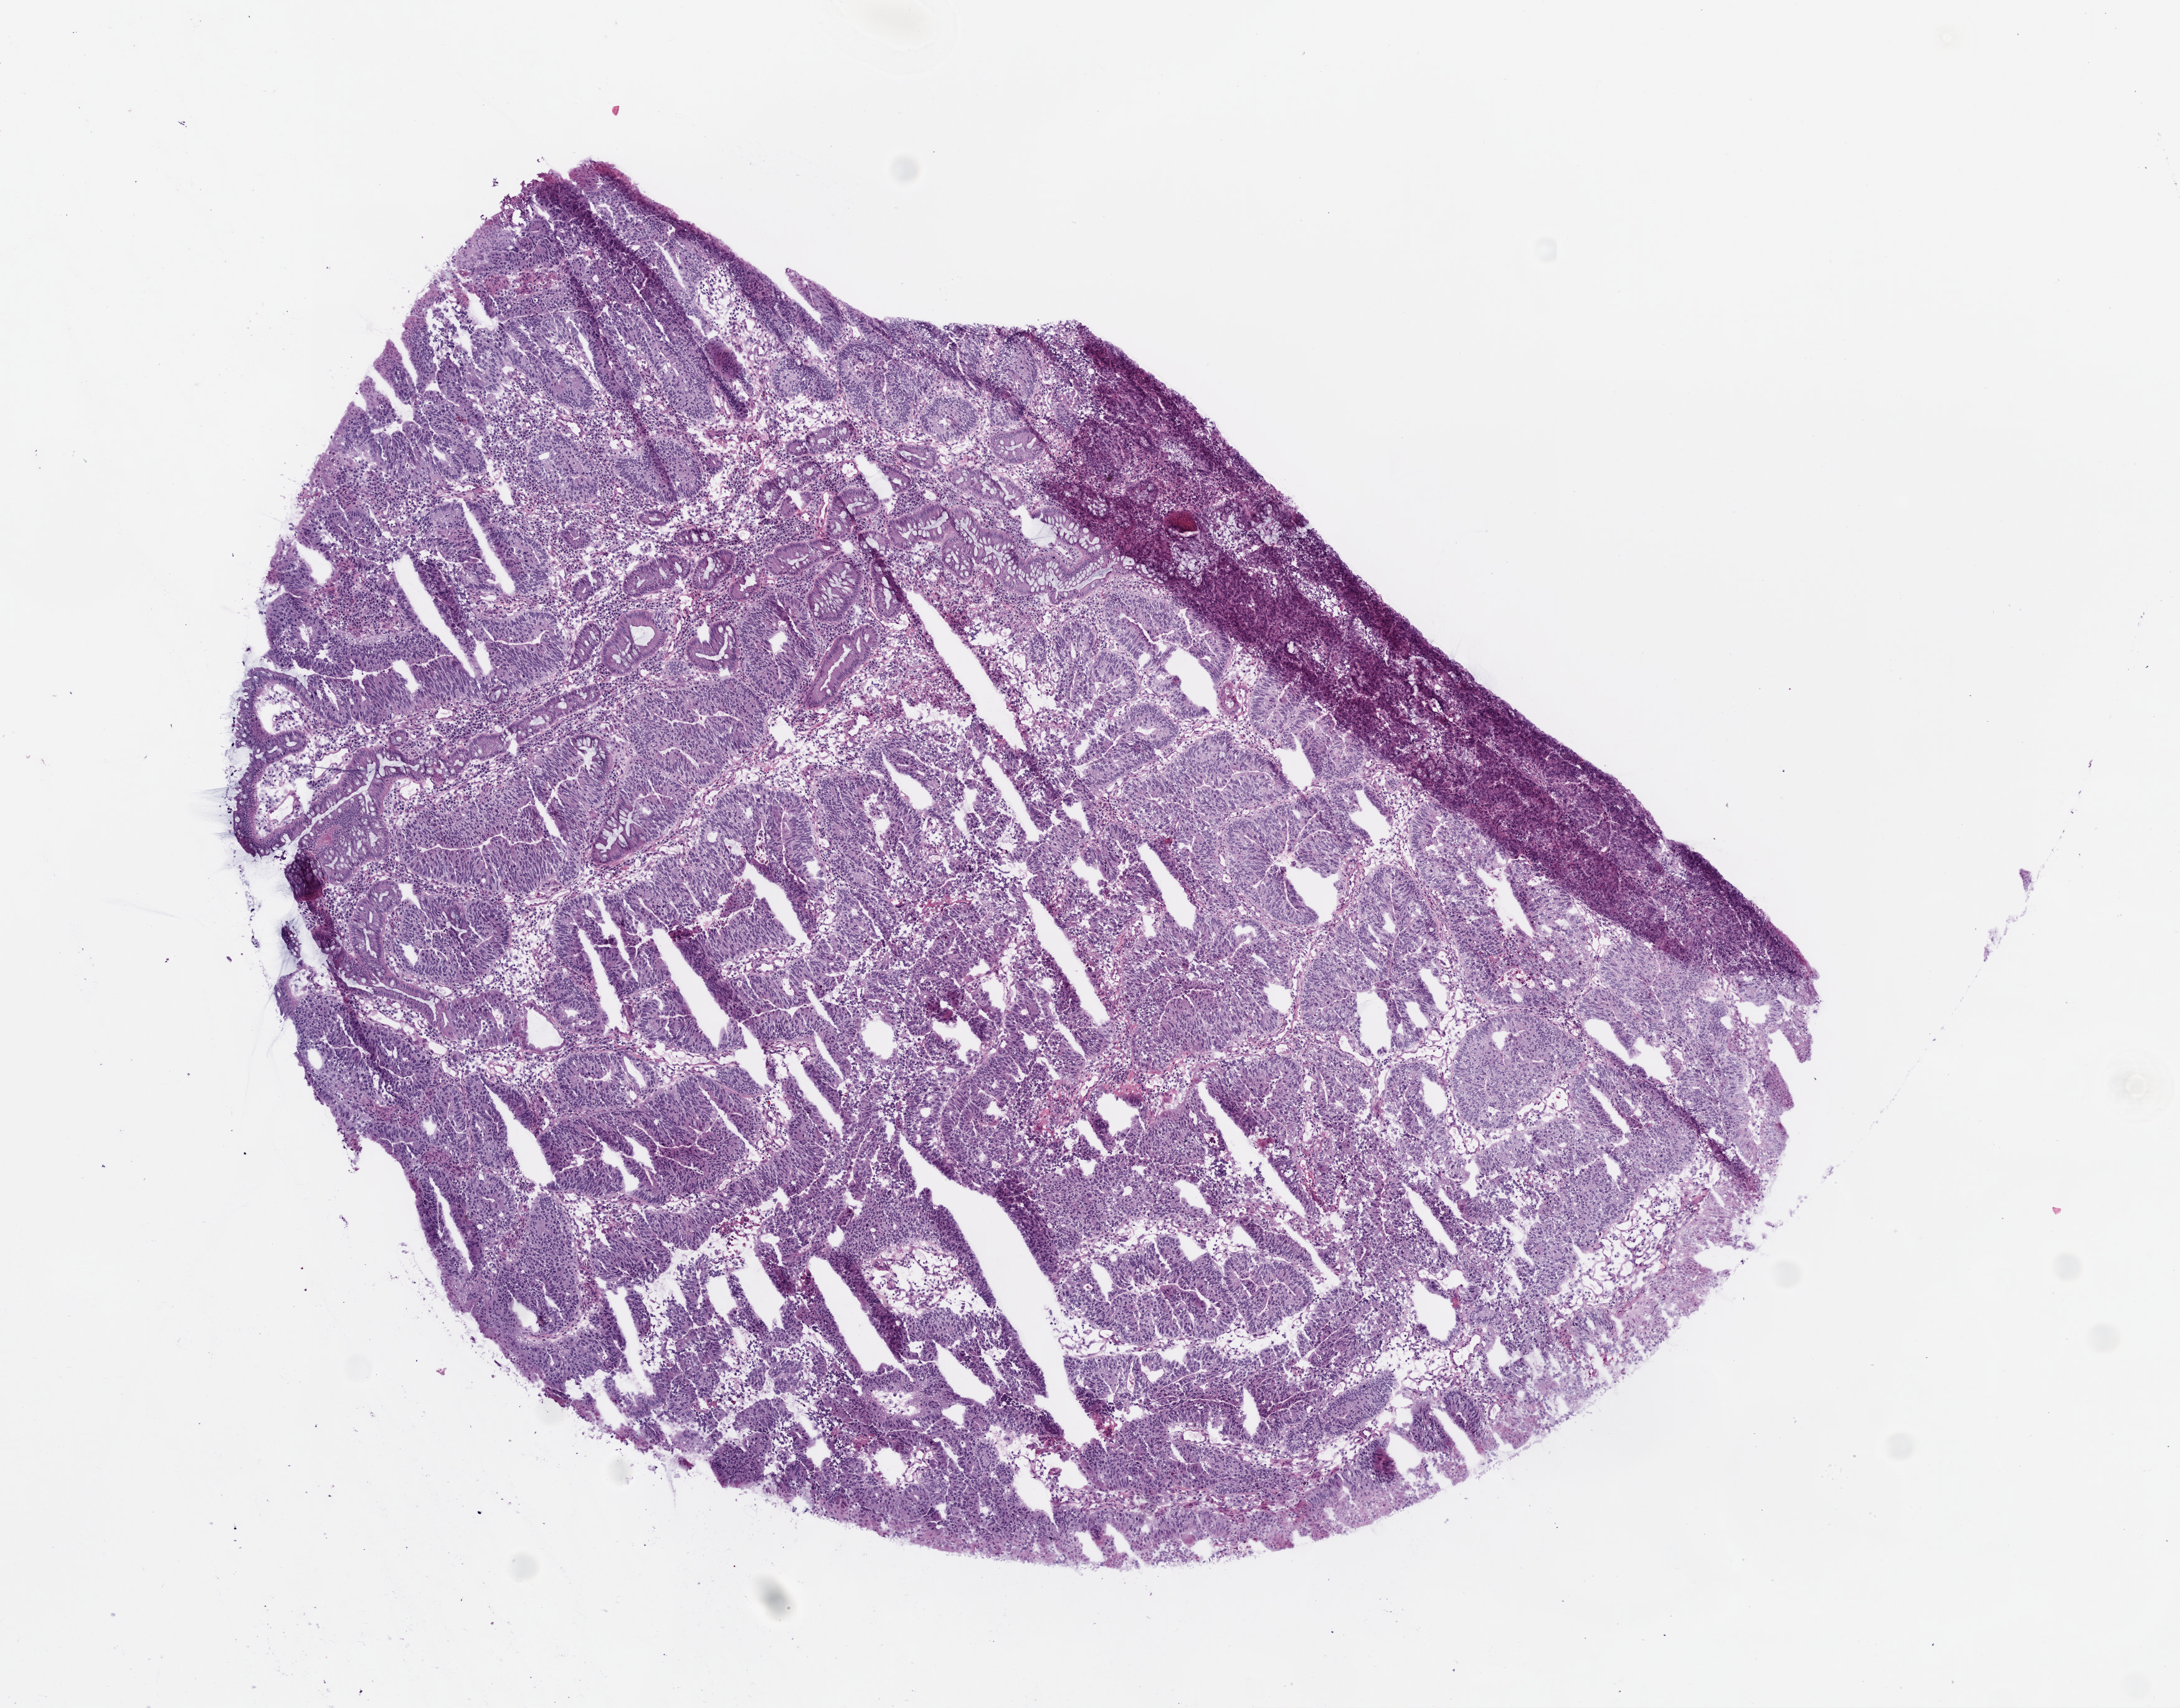
H&E-stained whole-slide image, whole scanned area (about 7.0 x 5.5 mm) shown as a low-resolution overview; frozen section from the bottom of the tissue portion; colon, primary tumour sample. Patient: male, age at initial diagnosis 58 years.
Pathologic diagnosis: Adenocarcinoma, NOS (rectosigmoid junction).